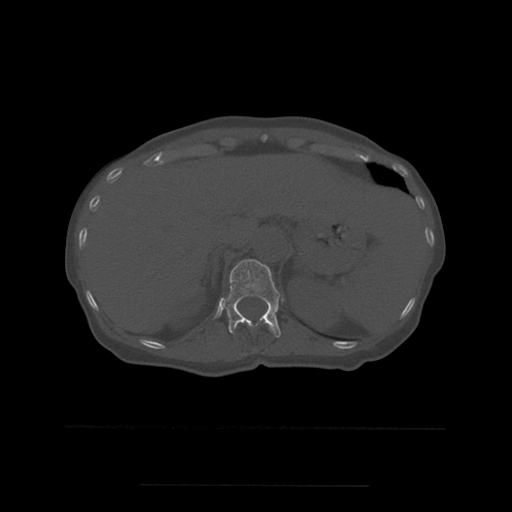
CT including the spine, one axial slice. Slice 263 of 544 in the series (ordered by position). Bone window (W 1800 / L 400 HU). 1.25 mm slice thickness. 512 × 512 image matrix. Patient age 58 years. Case-level facts recorded for this patient, not image findings: primary cancer: lung.
Outlined on this slice (semi-automatic segmentation, software-assisted and operator-edited):
- T11 vertebra: bounding box <240,321,266,323> (left, top, right, bottom; pixels)
- T12 vertebra: <223,259,283,338>